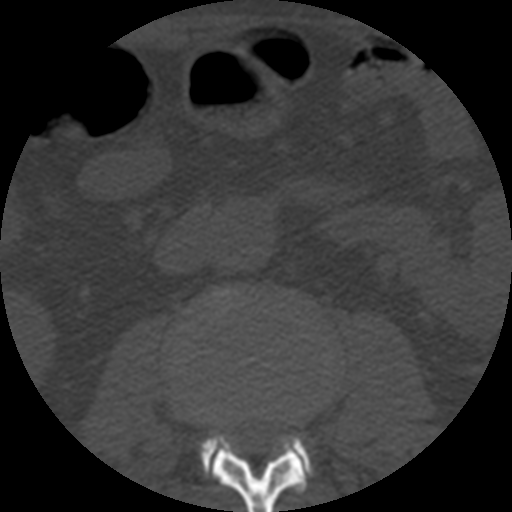
CT including the spine, one axial slice. Slice 139 of 508 in the series (ordered by position). Bone window (W 1800 / L 400 HU). 1.25 mm slice thickness. 512 × 512 image matrix. Patient age 57 years. Case-level facts recorded for this patient, not image findings: primary cancer: prostate.
Annotated regions visible in this slice (semi-automatic segmentation, software-assisted and operator-edited):
- L2 vertebra: bounding box <202,434,309,512> (left, top, right, bottom; pixels)
- L3 vertebra: <202,437,303,470>